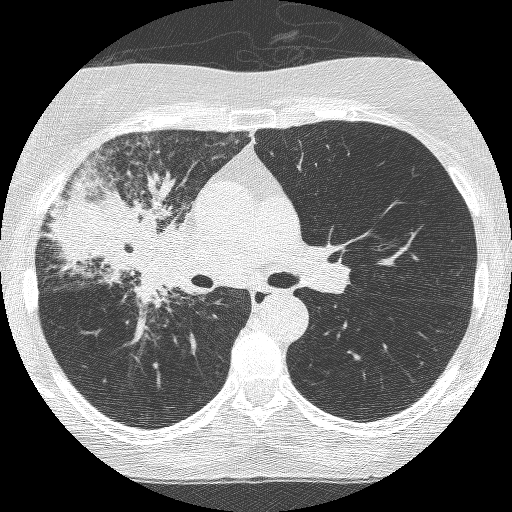
Axial slice from a low-dose chest CT screening exam. Third annual screen. Lung window (W 1500 / L -600 HU). 1.25 mm slice thickness. 120 kVp. Slice 156 of 253 in the series. 512 × 512 image matrix, field of view 294 × 294 mm. Female, age 64 years at enrolment. Former smoker at enrolment.
Expert-annotated lung lesion, bounding box (x1, y1, x2, y2) in pixels: (75, 194, 203, 323). Screening reader's record for this exam (one nodule recorded; not confirmed to be the boxed lesion): non-calcified nodule or mass ≥4 mm, right upper lobe, 49 × 43 mm, spiculated (stellate) margins, soft tissue attenuation, pre-existing on the prior screen: yes; interval growth: yes. Participant outcome: lung cancer diagnosed 7 days after this screen — adenocarcinoma, NOS, right upper lobe, right middle lobe, right hilum, stage IV (AJCC 6th edition), 85 mm at pathology.